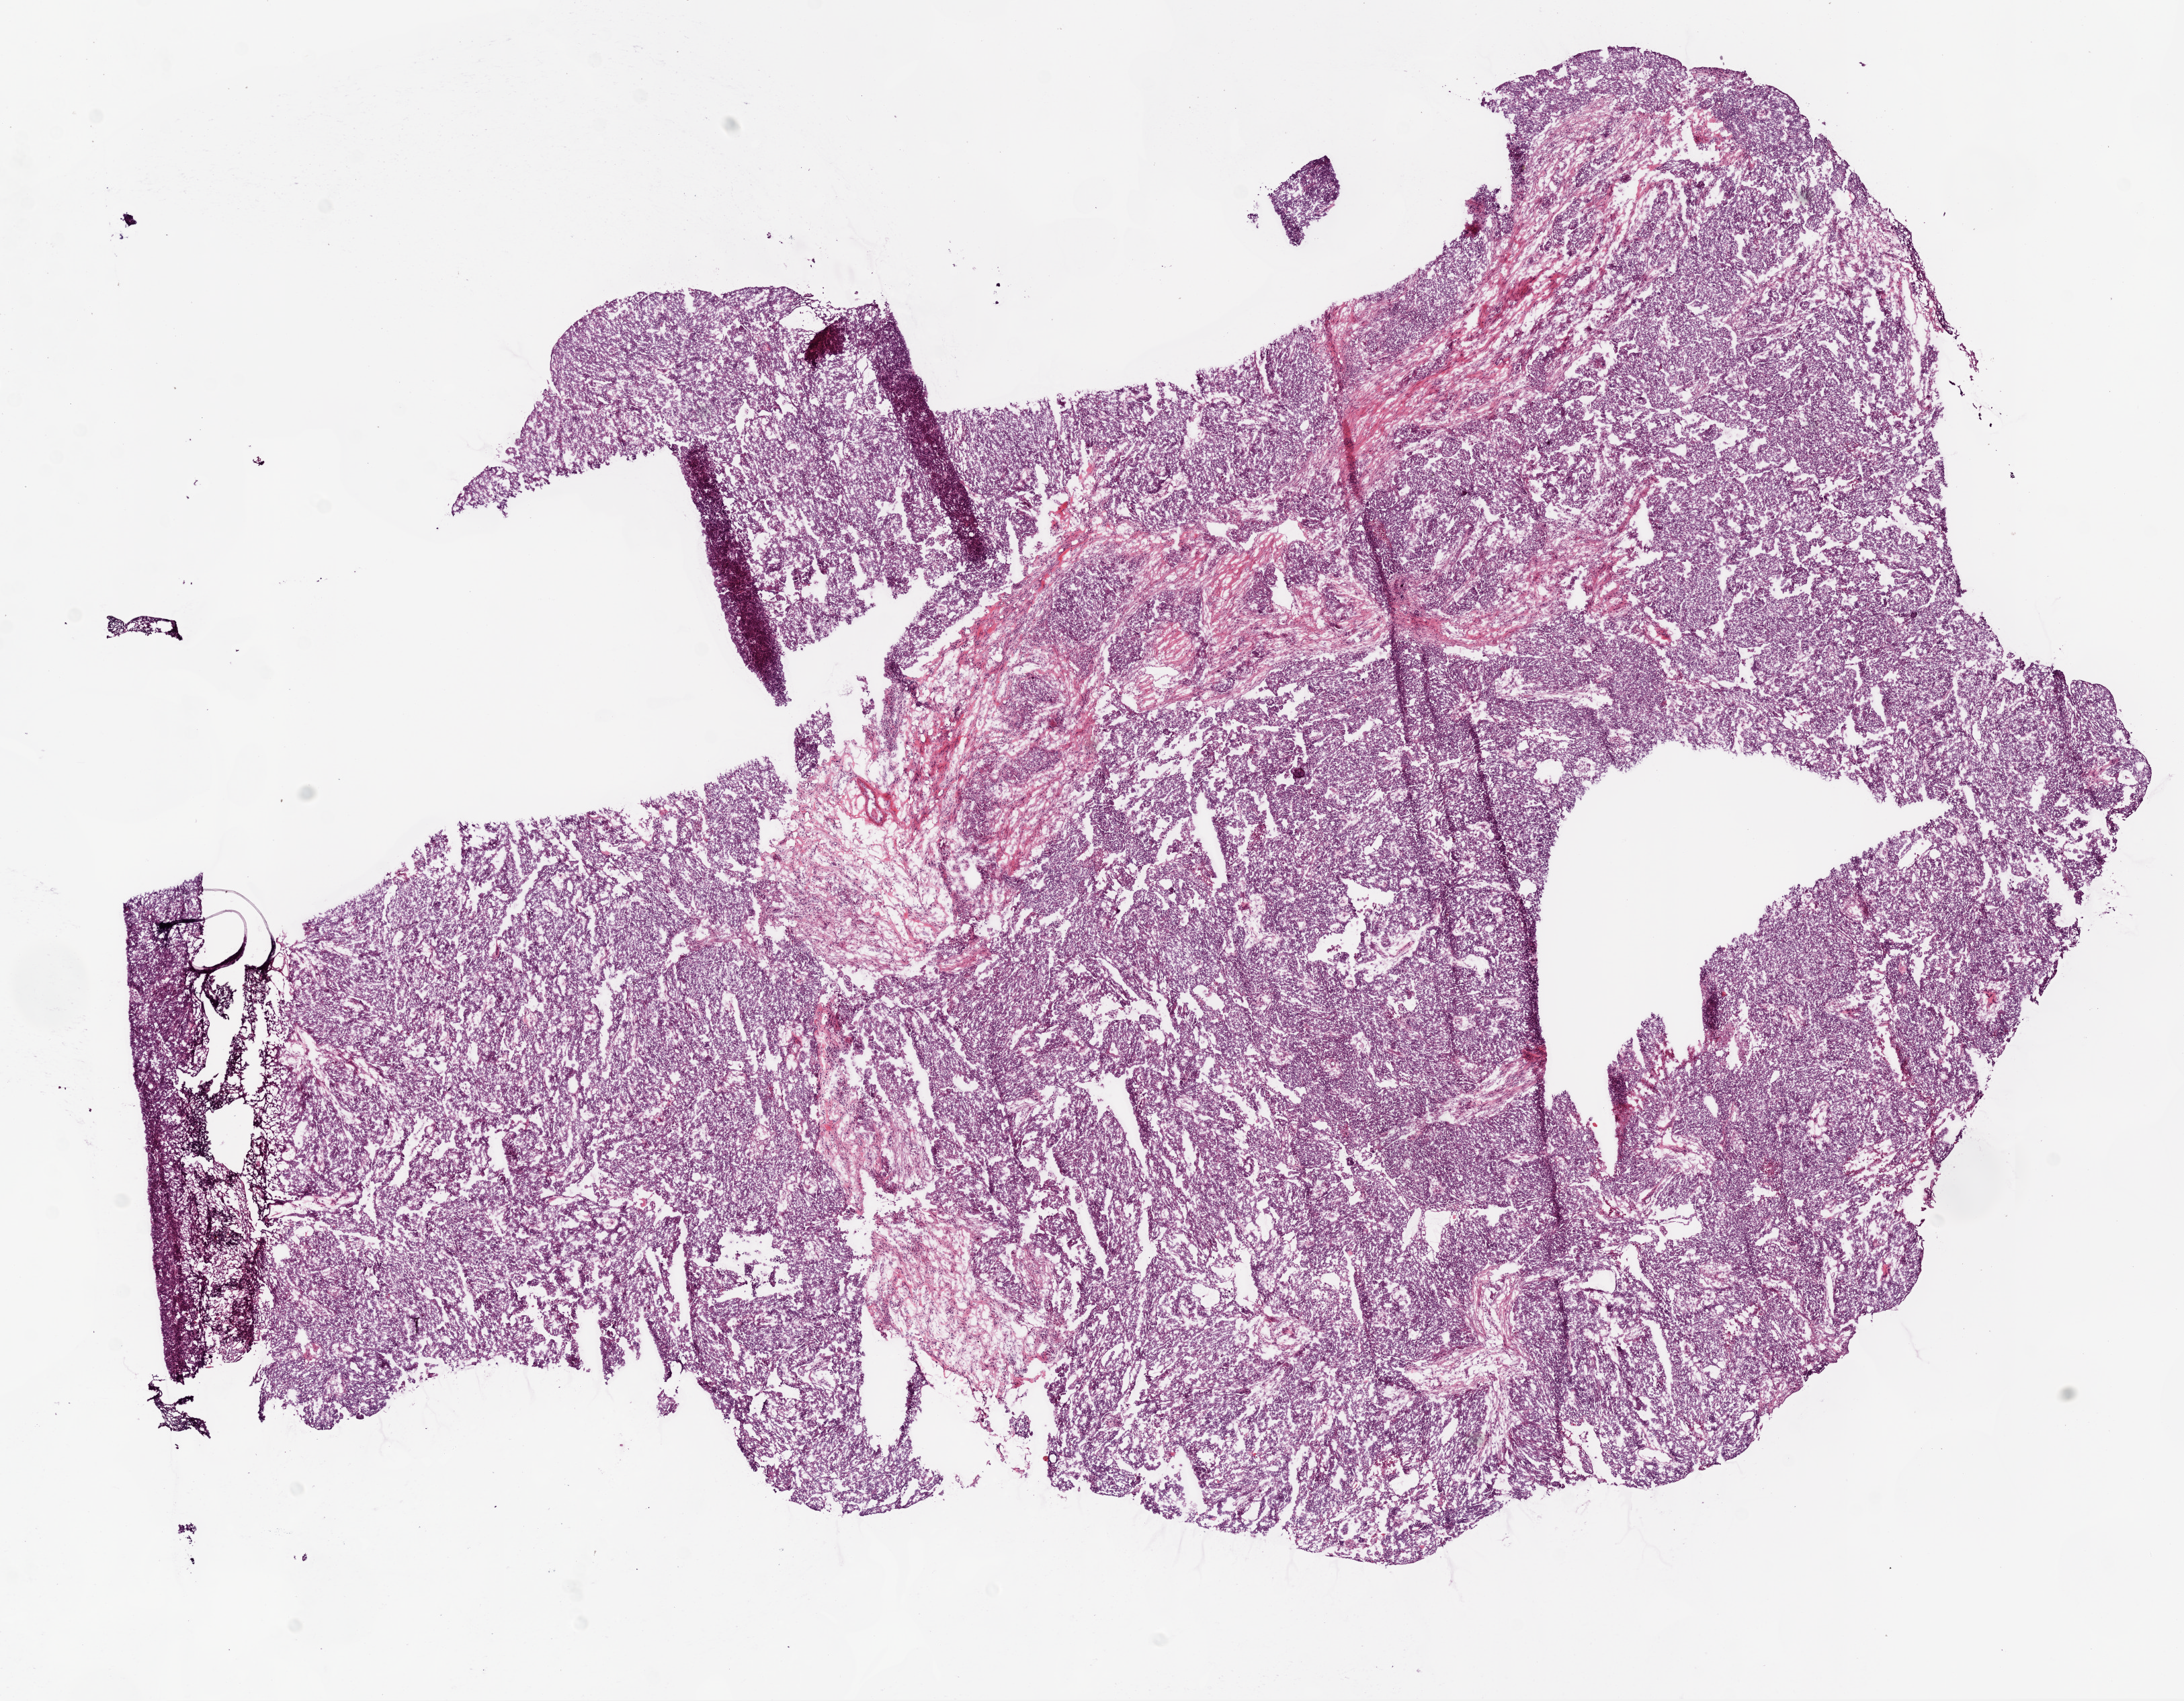
H&E-stained whole-slide image, shown as a low-resolution overview of the whole scanned area (about 13.0 x 10.2 mm); frozen section; sample: primary tumour, ovary. Patient: female, age at initial diagnosis 55 years. Composition of this section per pathologist review: tumour cells 90%, tumour nuclei 80%.
Histologic diagnosis: Serous cystadenocarcinoma, NOS.